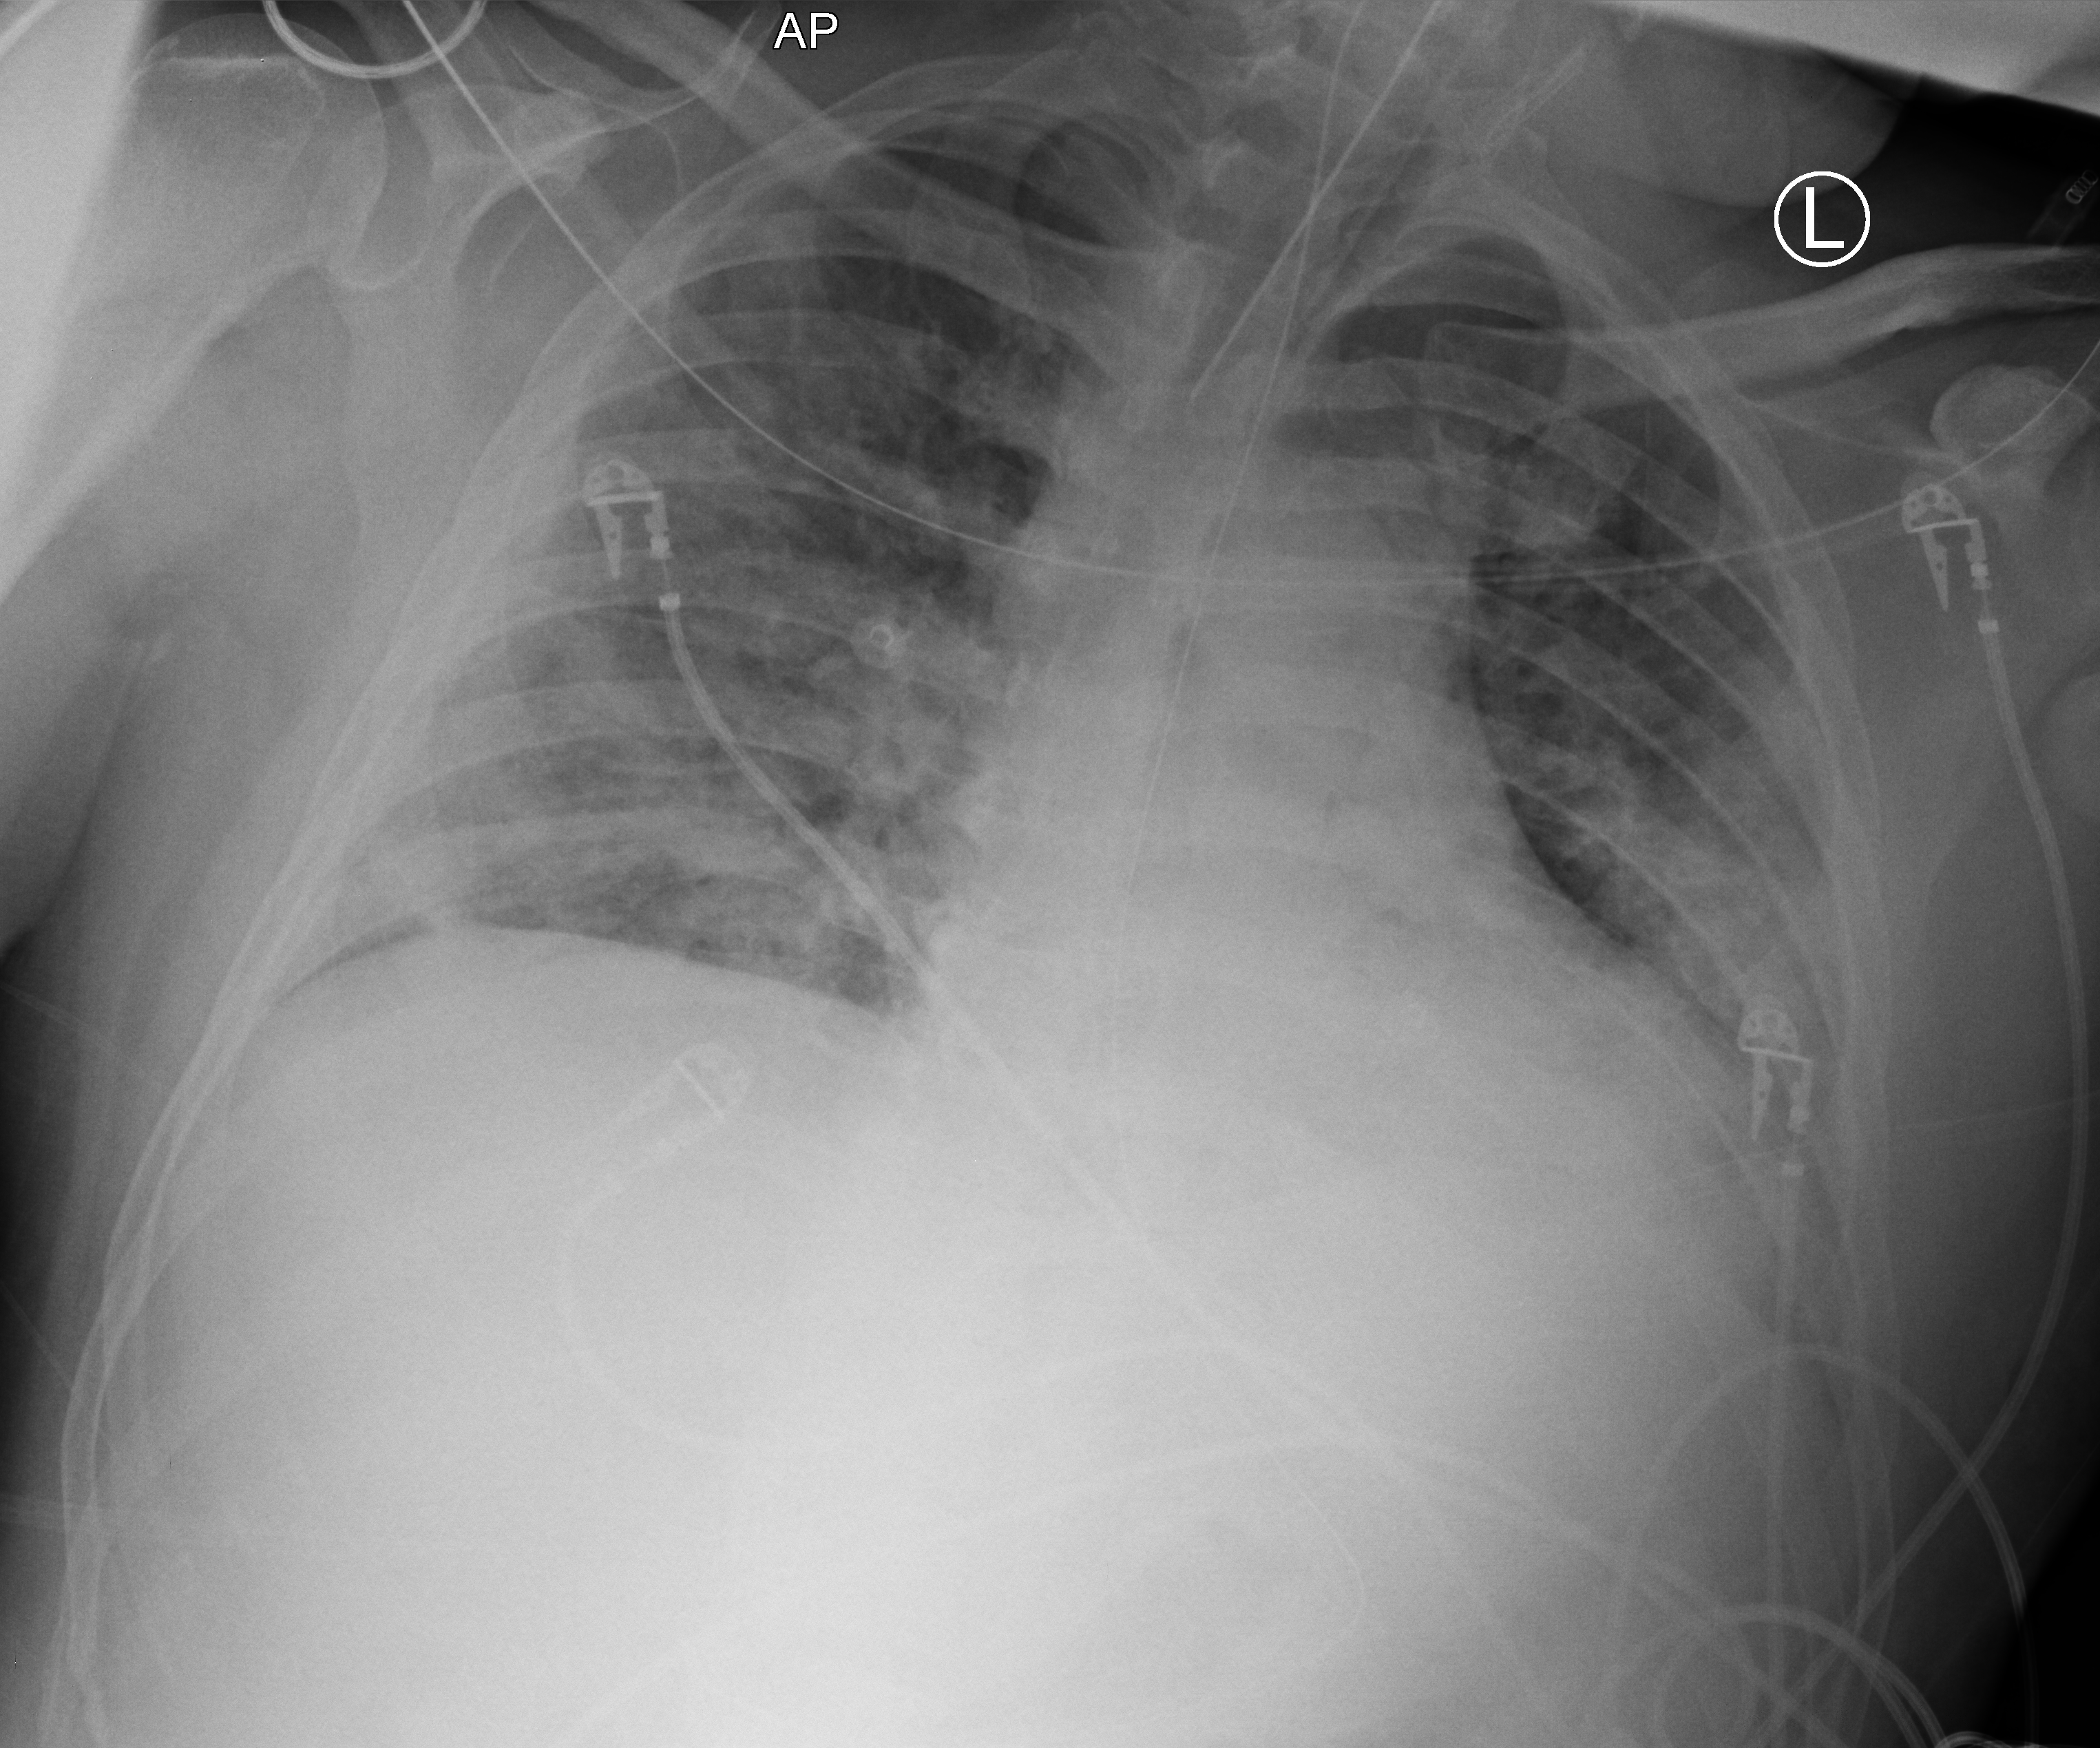
Portable chest radiograph; anteroposterior (AP) projection. Patient hospitalised with COVID-19; male, aged 18–59 years.
From the hospital-stay record, not from the radiograph (when in the stay this image was taken is not recorded):
- other chronic lung disease (admission record): no
- mechanically ventilated during this hospital stay: yes
- hypertension (admission record): yes